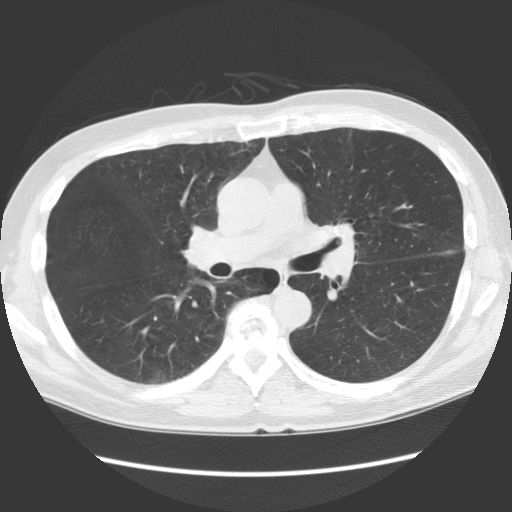
Low-dose screening chest CT, one axial slice; position 75 of 136 along the scan axis; 140 kVp; lung window (W 1500 / L -600 HU); 2.5 mm slice thickness; 512 × 512 image matrix, field of view 360 × 360 mm.
Structures marked on this image (expert manual segmentation):
- lesion 1 (tumor, hilum of left lung): bounding box [x1, y1, x2, y2] px = [333, 223, 355, 251]